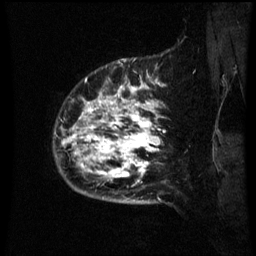
Breast MRI (dynamic contrast-enhanced), one sagittal slice; slice 56 of 60 in the series (ordered by position); dynamic contrast-enhanced series, image 2 of 3 at this slice position (ordered by acquisition); 1.5 T; TE 4.2 ms, TR 8.9 ms; 2.1 mm slice thickness; 256 × 256 image matrix, field of view 200 × 200 mm. Patient: female, 42 years. From the clinical record (not read from this slice): setting: breast cancer imaged before/during neoadjuvant chemotherapy; receptor status: HER2-positive.
Annotated regions visible in this slice (semi-automatic segmentation, software-assisted and operator-edited):
- analysis volume of interest (the breast-tissue region the enhancement analysis was run in; not a lesion): bounding box <66,82,169,193> (left, top, right, bottom; pixels)
- tumour enhancement mask (voxels above the 70 % enhancement threshold inside the analysis volume of interest): <66,84,161,183>